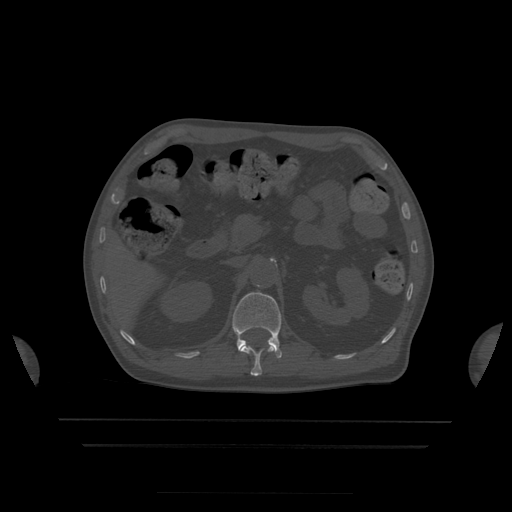
CT including the spine, one axial slice; slice 181 of 522 in the series (ordered by position); bone window (W 1800 / L 400 HU); 512 × 512 image matrix, field of view 436 × 436 mm. Patient age 68 years. From the clinical record (not read from this slice): primary cancer: urothelial.
Structures marked on this image (semi-automatic segmentation, software-assisted and operator-edited):
- L1 vertebra: bounding box (x1, y1, x2, y2) in pixels: (232, 293, 283, 358)
- T12 vertebra: (241, 345, 275, 376)